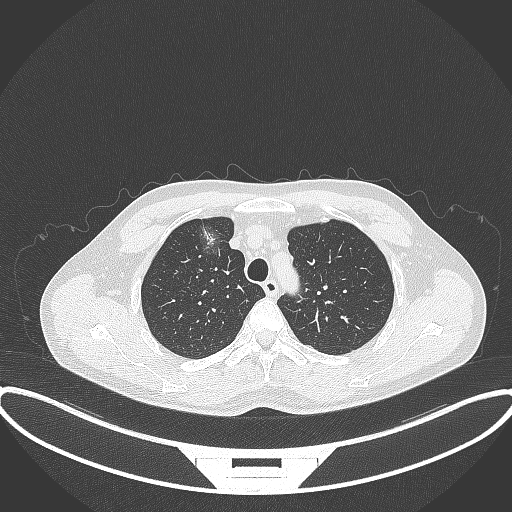
Chest CT, one axial slice. Slice 290 of 395 in the series (ordered by position). Reconstruction kernel B70f. Lung window (W 1500 / L -600 HU). 1 mm slice thickness. 512 × 512 image matrix, field of view 424 × 424 mm. Patient: male, 60 years. From the clinical record (not read from this slice): clinical TNM (as recorded): T1c N0 M0.
Annotated regions visible in this slice (bounding box drawn by a radiologist):
- lung tumour (recorded histology: adenocarcinoma): bounding box (x1, y1, x2, y2) in pixels: (190, 214, 228, 261)